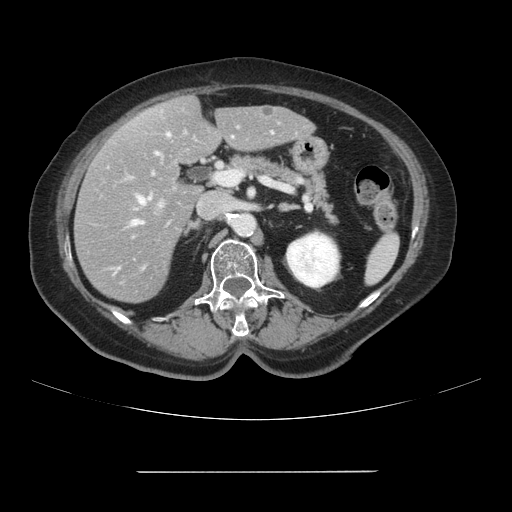
Contrast-enhanced abdominal CT, one axial slice. Intravenous contrast given. Soft-tissue window (W 400 / L 40 HU). 2.5 mm slice thickness. 512 × 512 image matrix, field of view 400 × 400 mm. Female patient, age 74 years. Case-level facts recorded for this patient, not image findings: diagnosis: colorectal cancer liver metastases, imaged before liver resection; multiple liver metastases: yes; largest metastasis: 1.1 cm; chemotherapy before resection: yes.
Annotated regions visible in this slice (expert manual segmentation):
- hepatic veins: bounding box (x1, y1, x2, y2) in pixels: (132, 134, 169, 225)
- liver: (75, 97, 313, 302)
- planned liver remnant (the part of the liver to remain after resection): (143, 97, 314, 165)
- portal vein (with intrahepatic branches): (126, 120, 282, 210)
- liver metastasis: (262, 106, 271, 114)